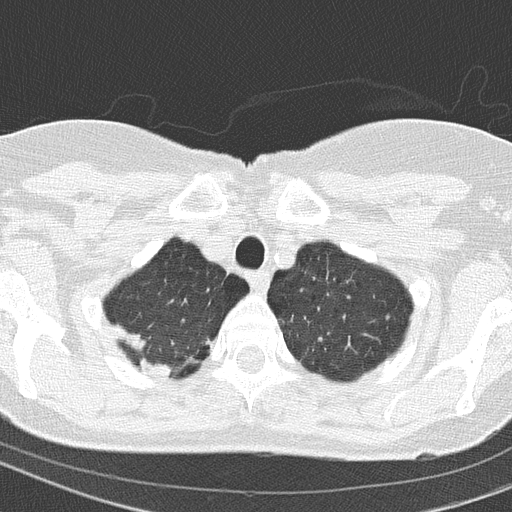
Low-dose screening chest CT, one axial slice; slice 136 of 154 in the series (ordered by position); 120 kVp; lung window (W 1500 / L -600 HU); 2 mm slice thickness; 512 × 512 image matrix, field of view 288 × 288 mm.
Annotated regions visible in this slice (outlined manually by an expert reader):
- lesion 1 (tumor, upper lobe of right lung): bounding box <140,358,172,378> (left, top, right, bottom; pixels)